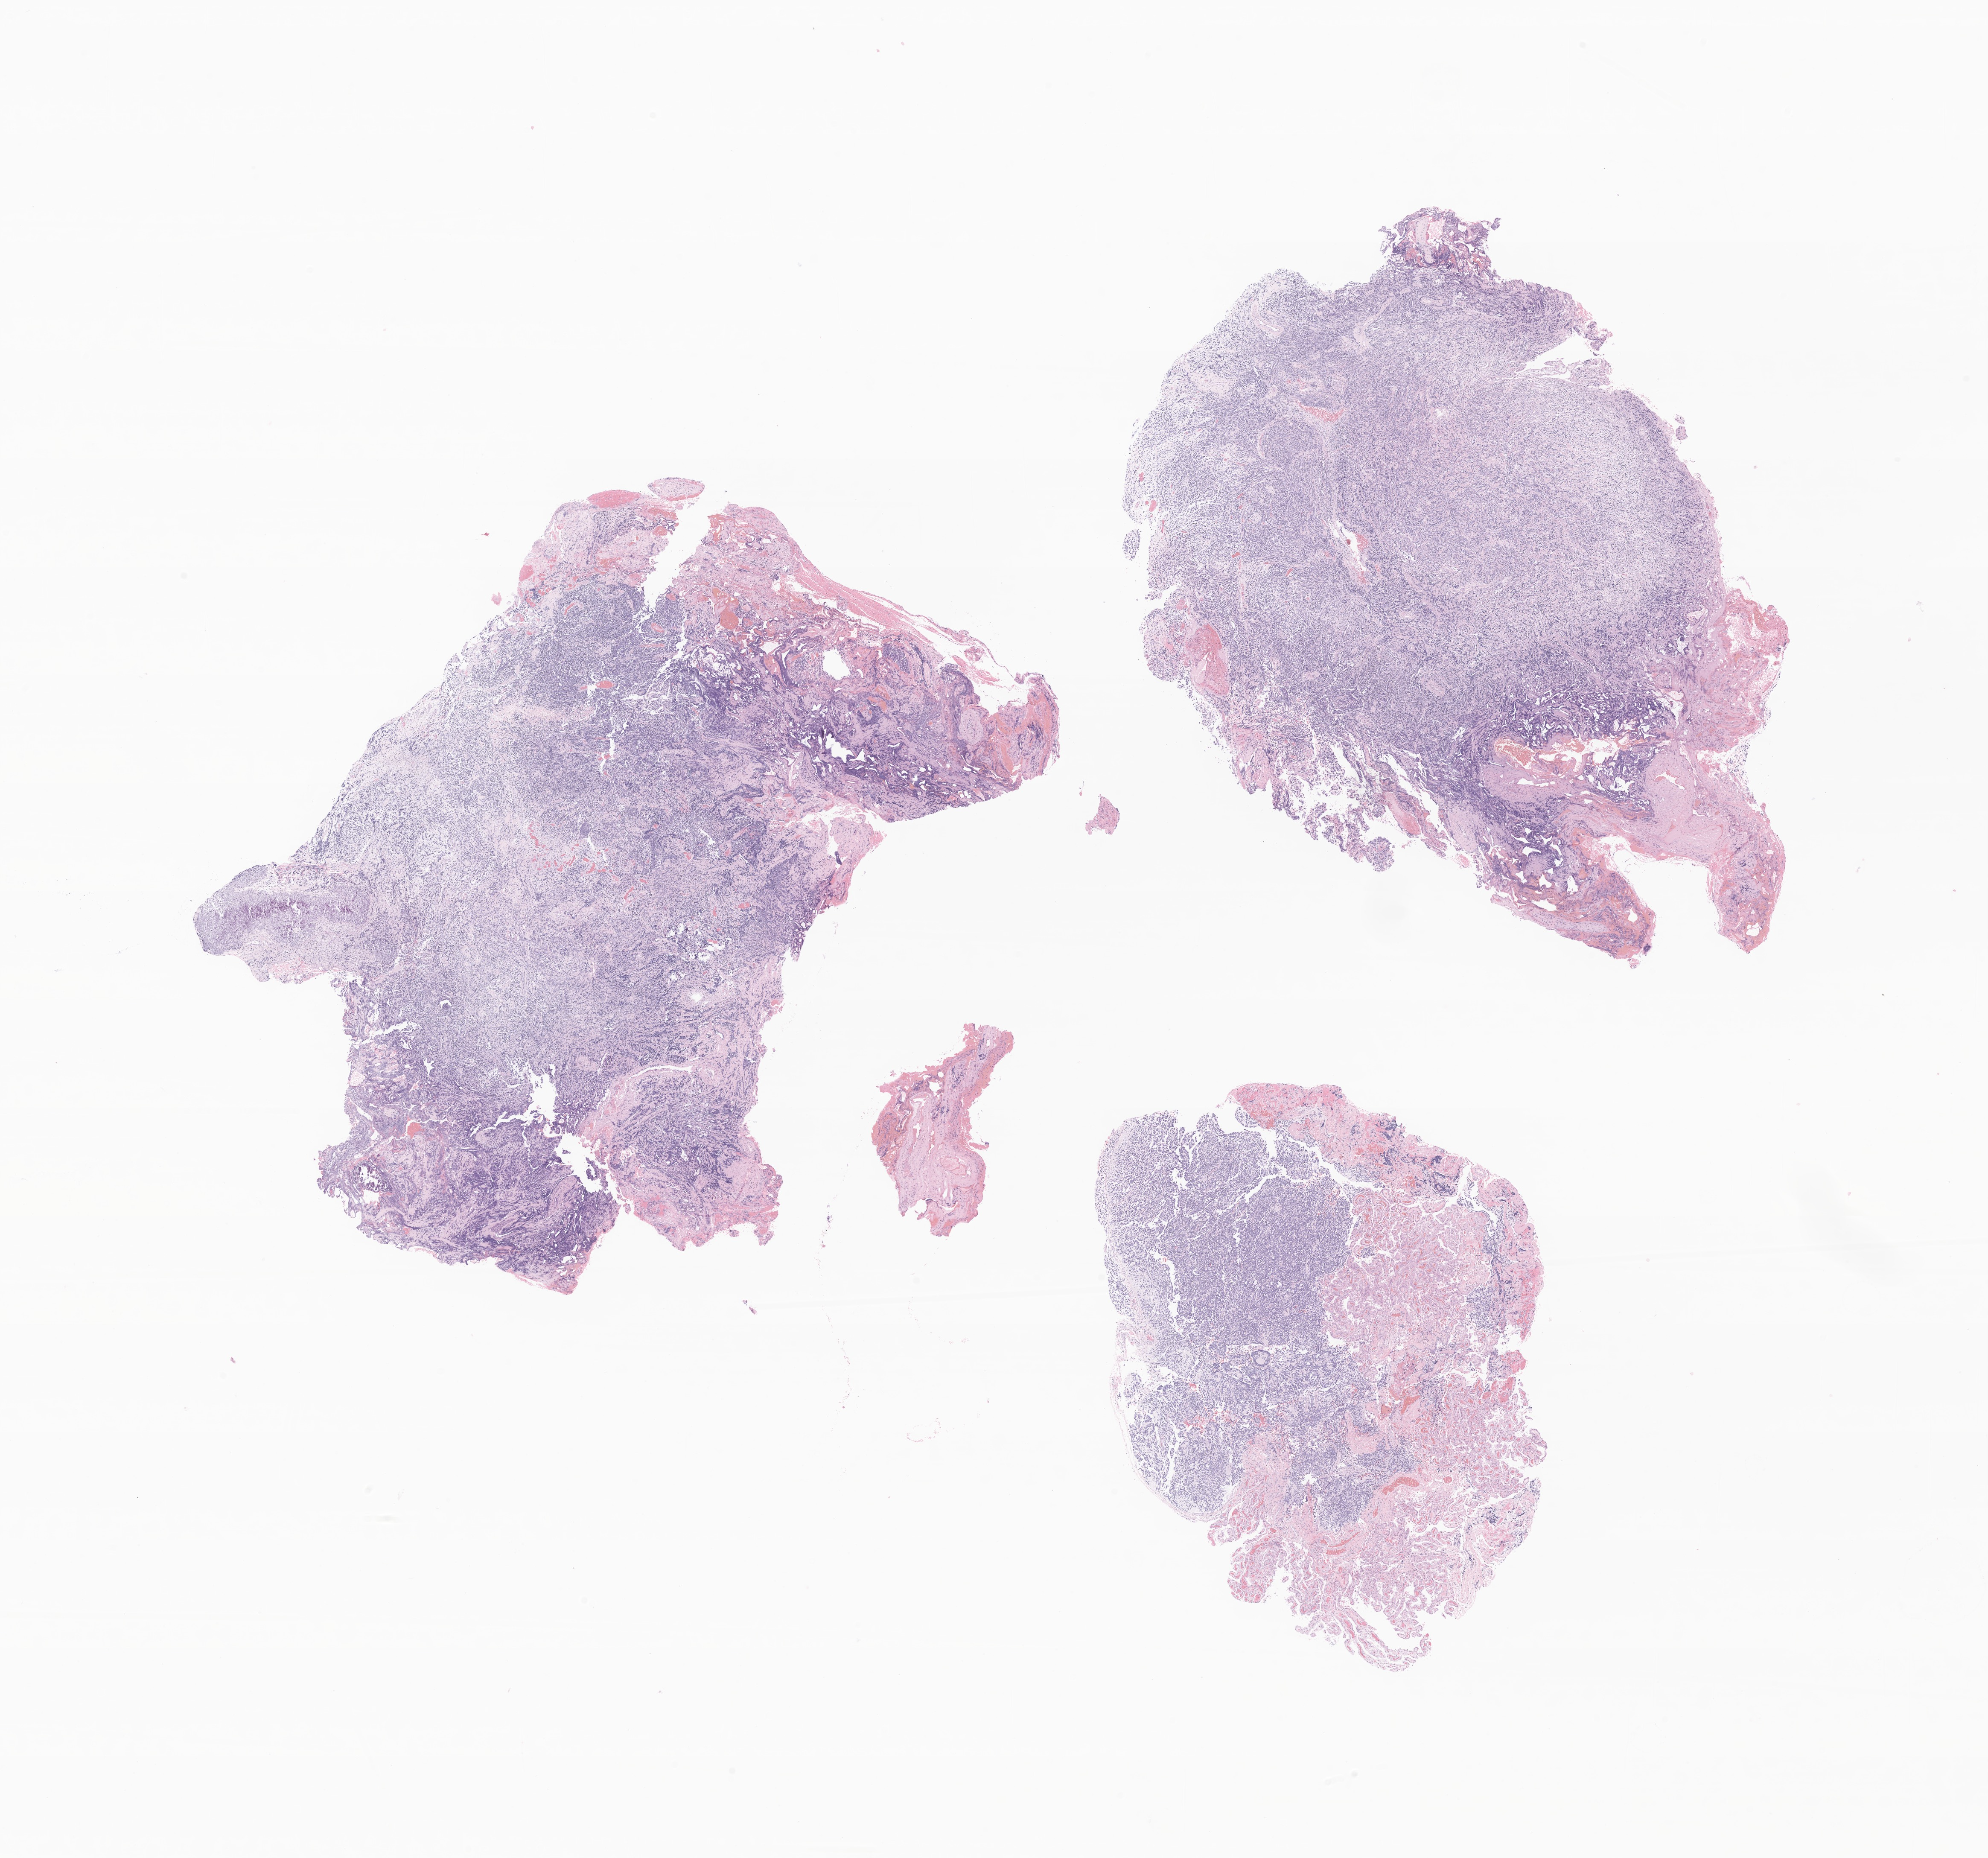
H&E whole-slide image of tumor tissue from the brain — low-resolution overview of the scanned area, about 19.6 x 18.4 mm; FFPE section. Patient female; age 112 months (9 years 4 months).
* diagnosis (ICD-O-3 morphology term): Medulloblastoma, NOS